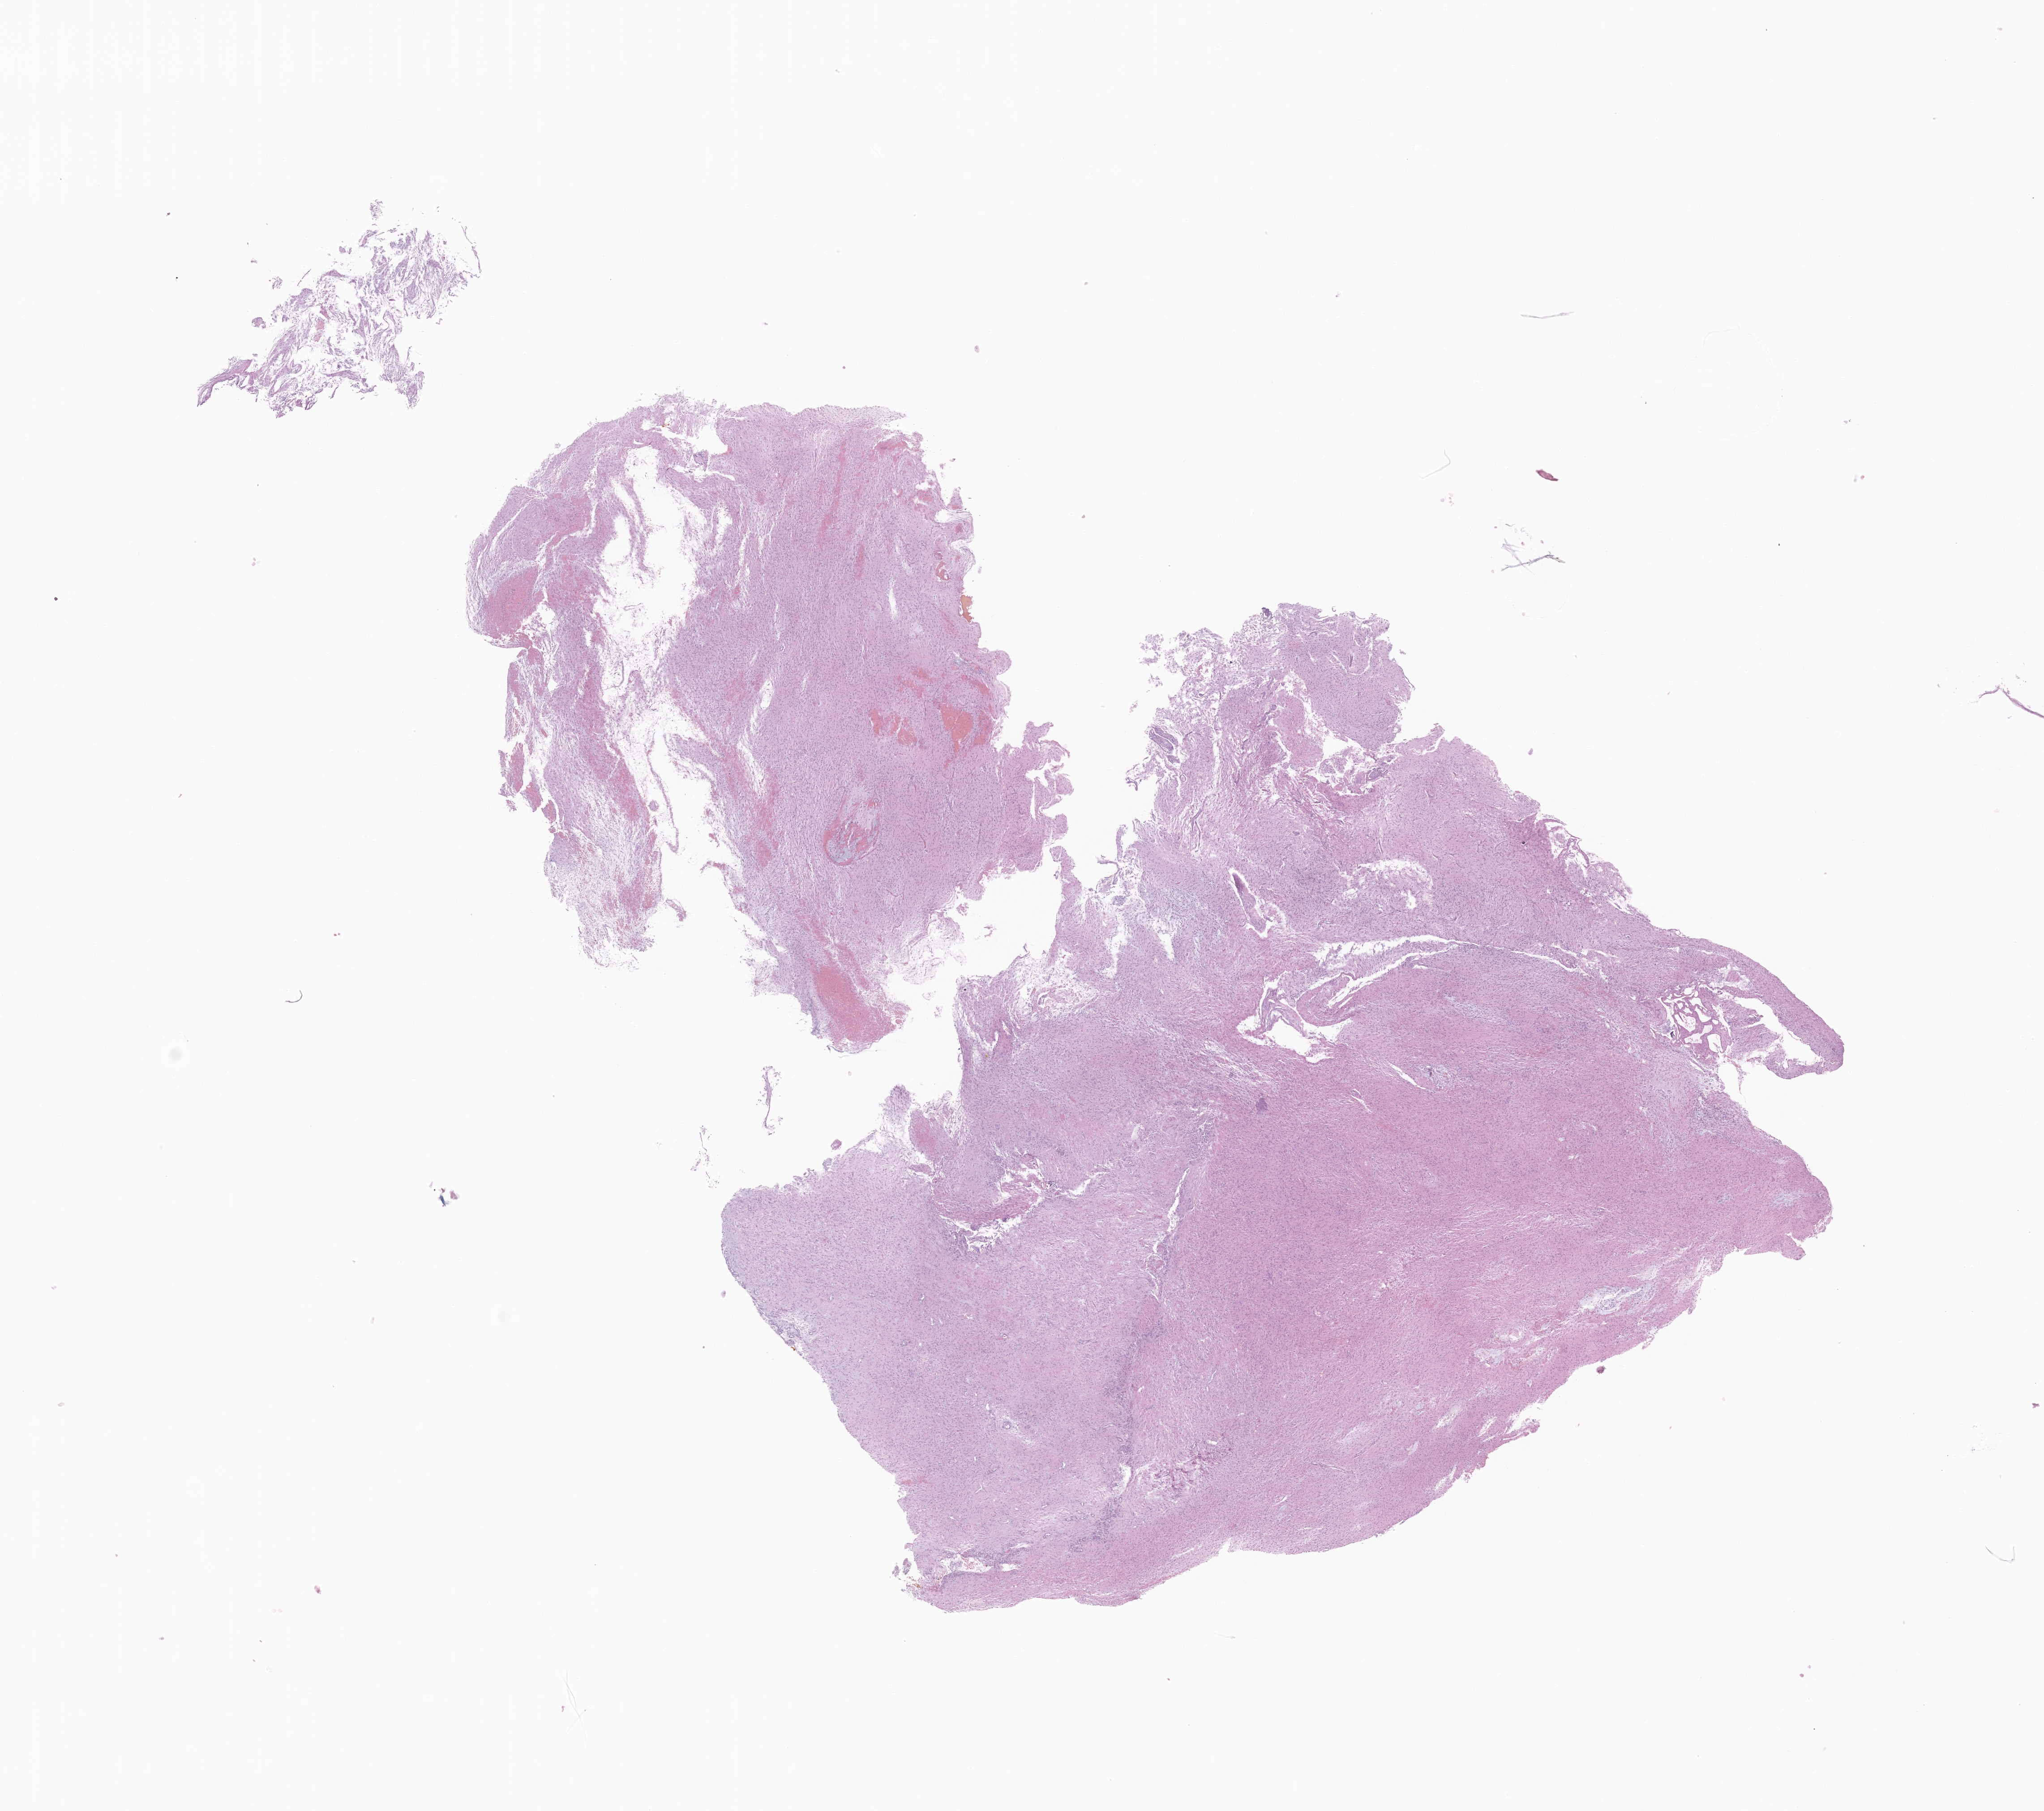
Digitized H&E-stained section of tumor tissue from the central nervous system, low-resolution overview of the scanned area, about 19.2 x 17.0 mm. Formalin-fixed, paraffin-embedded (FFPE) tissue. Patient male; age 81 months (6 years 9 months).
Diagnosis (ICD-O-3 morphology term): Neoplasm, uncertain whether benign or malignant.